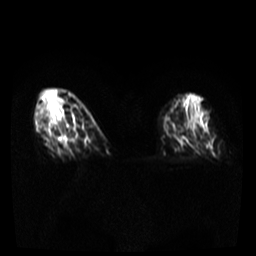
Breast MRI, one axial slice; position 13 of 36 along the scan axis; diffusion-weighted series; image 2 of 4 stored at this slice position (different b-values; order by instance number); 3 T; 5 mm slice thickness; 256 × 256 image matrix, field of view 300 × 300 mm. Female patient.
Structures marked on this image (manually delineated by an expert):
- tumour on diffusion-weighted imaging: box from (x=40, y=112) to (x=67, y=144) px